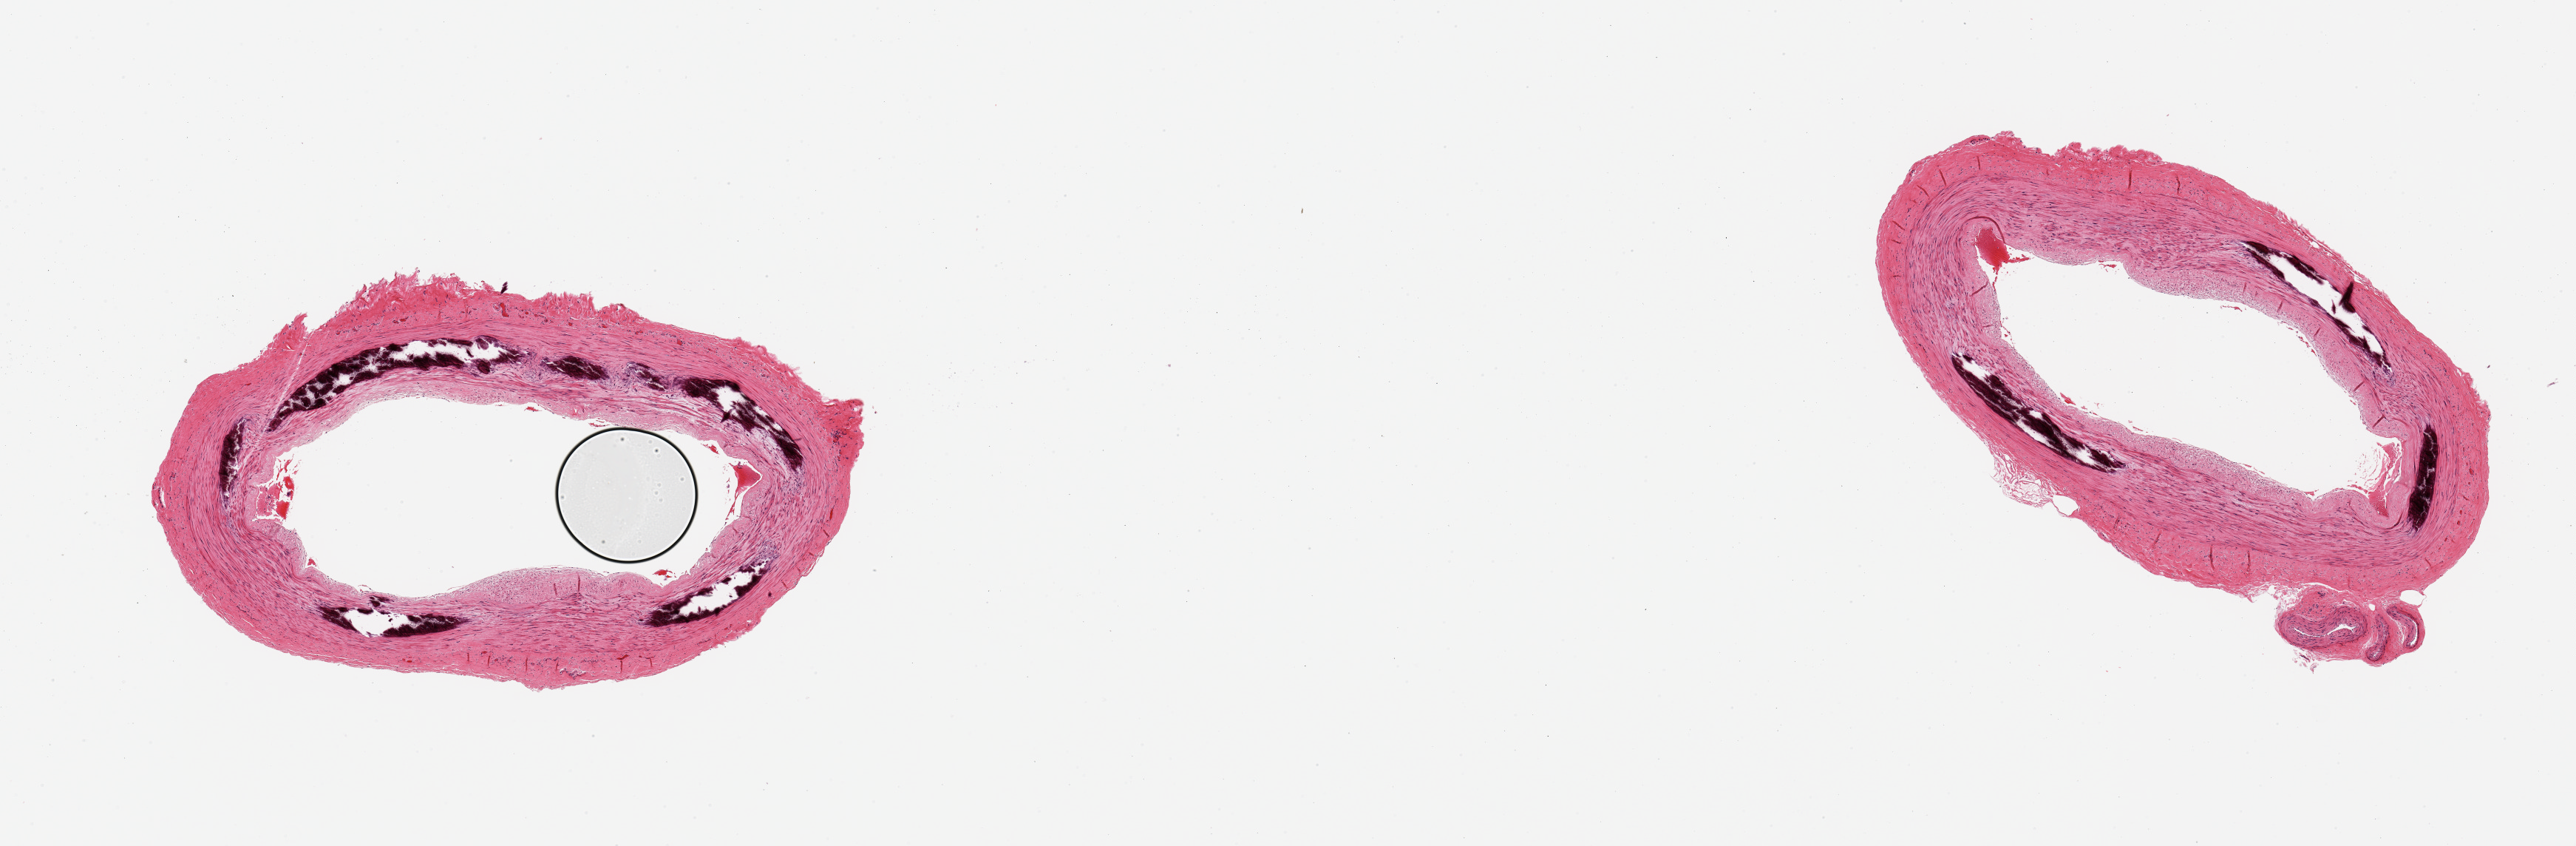
H&E whole-slide image, brightfield — a low-resolution overview of the entire scanned area, about 13.8 x 4.5 mm; PAXgene-fixed, paraffin-embedded tissue; target tissue: tibial artery; tissue donor sample. Donor: male.
Reviewer comment on this tissue sample: 2 pieces; significant medial calcifications and atheromatous plaque with luminal obliteration (less than 25%).